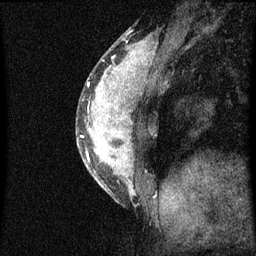
Breast MRI (dynamic contrast-enhanced), one sagittal slice; position 22 of 60 along the scan axis; dynamic contrast-enhanced series, image 2 of 3 at this slice position (ordered by acquisition); 1.5 T; TE 4.2 ms, TR 8 ms; 2 mm slice thickness; 256 × 256 image matrix, field of view 180 × 180 mm. Patient: female, 33 years.
Annotated regions visible in this slice (semi-automatically segmented with operator editing):
- analysis volume of interest (the breast-tissue region the enhancement analysis was run in; not a lesion): box from (x=76, y=56) to (x=152, y=203) px
- tumour enhancement mask (voxels above the 70 % enhancement threshold inside the analysis volume of interest): (x=81, y=60)–(x=136, y=193)